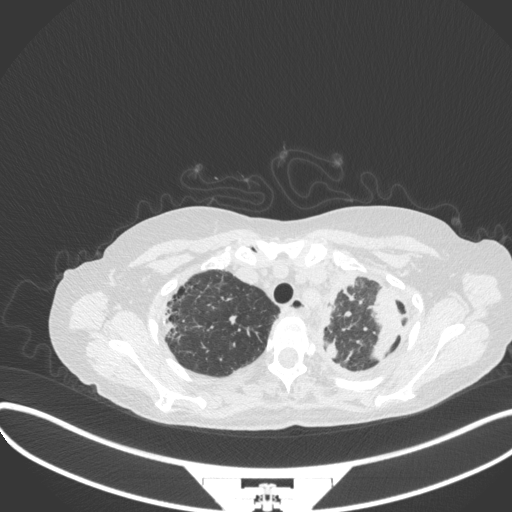
Chest CT, one axial slice; slice 284 of 373 in the series (ordered by position); lung window (W 1500 / L -600 HU); 1 mm slice thickness; 512 × 512 image matrix, field of view 400 × 400 mm. Patient: female, 56 years. From the clinical record (not read from this slice): clinical TNM (as recorded): T1 N0 M0.
Annotated regions visible in this slice (bounding box drawn by a radiologist):
- lung tumour (recorded histology: adenocarcinoma): bounding box [x1, y1, x2, y2] px = [366, 282, 399, 364]